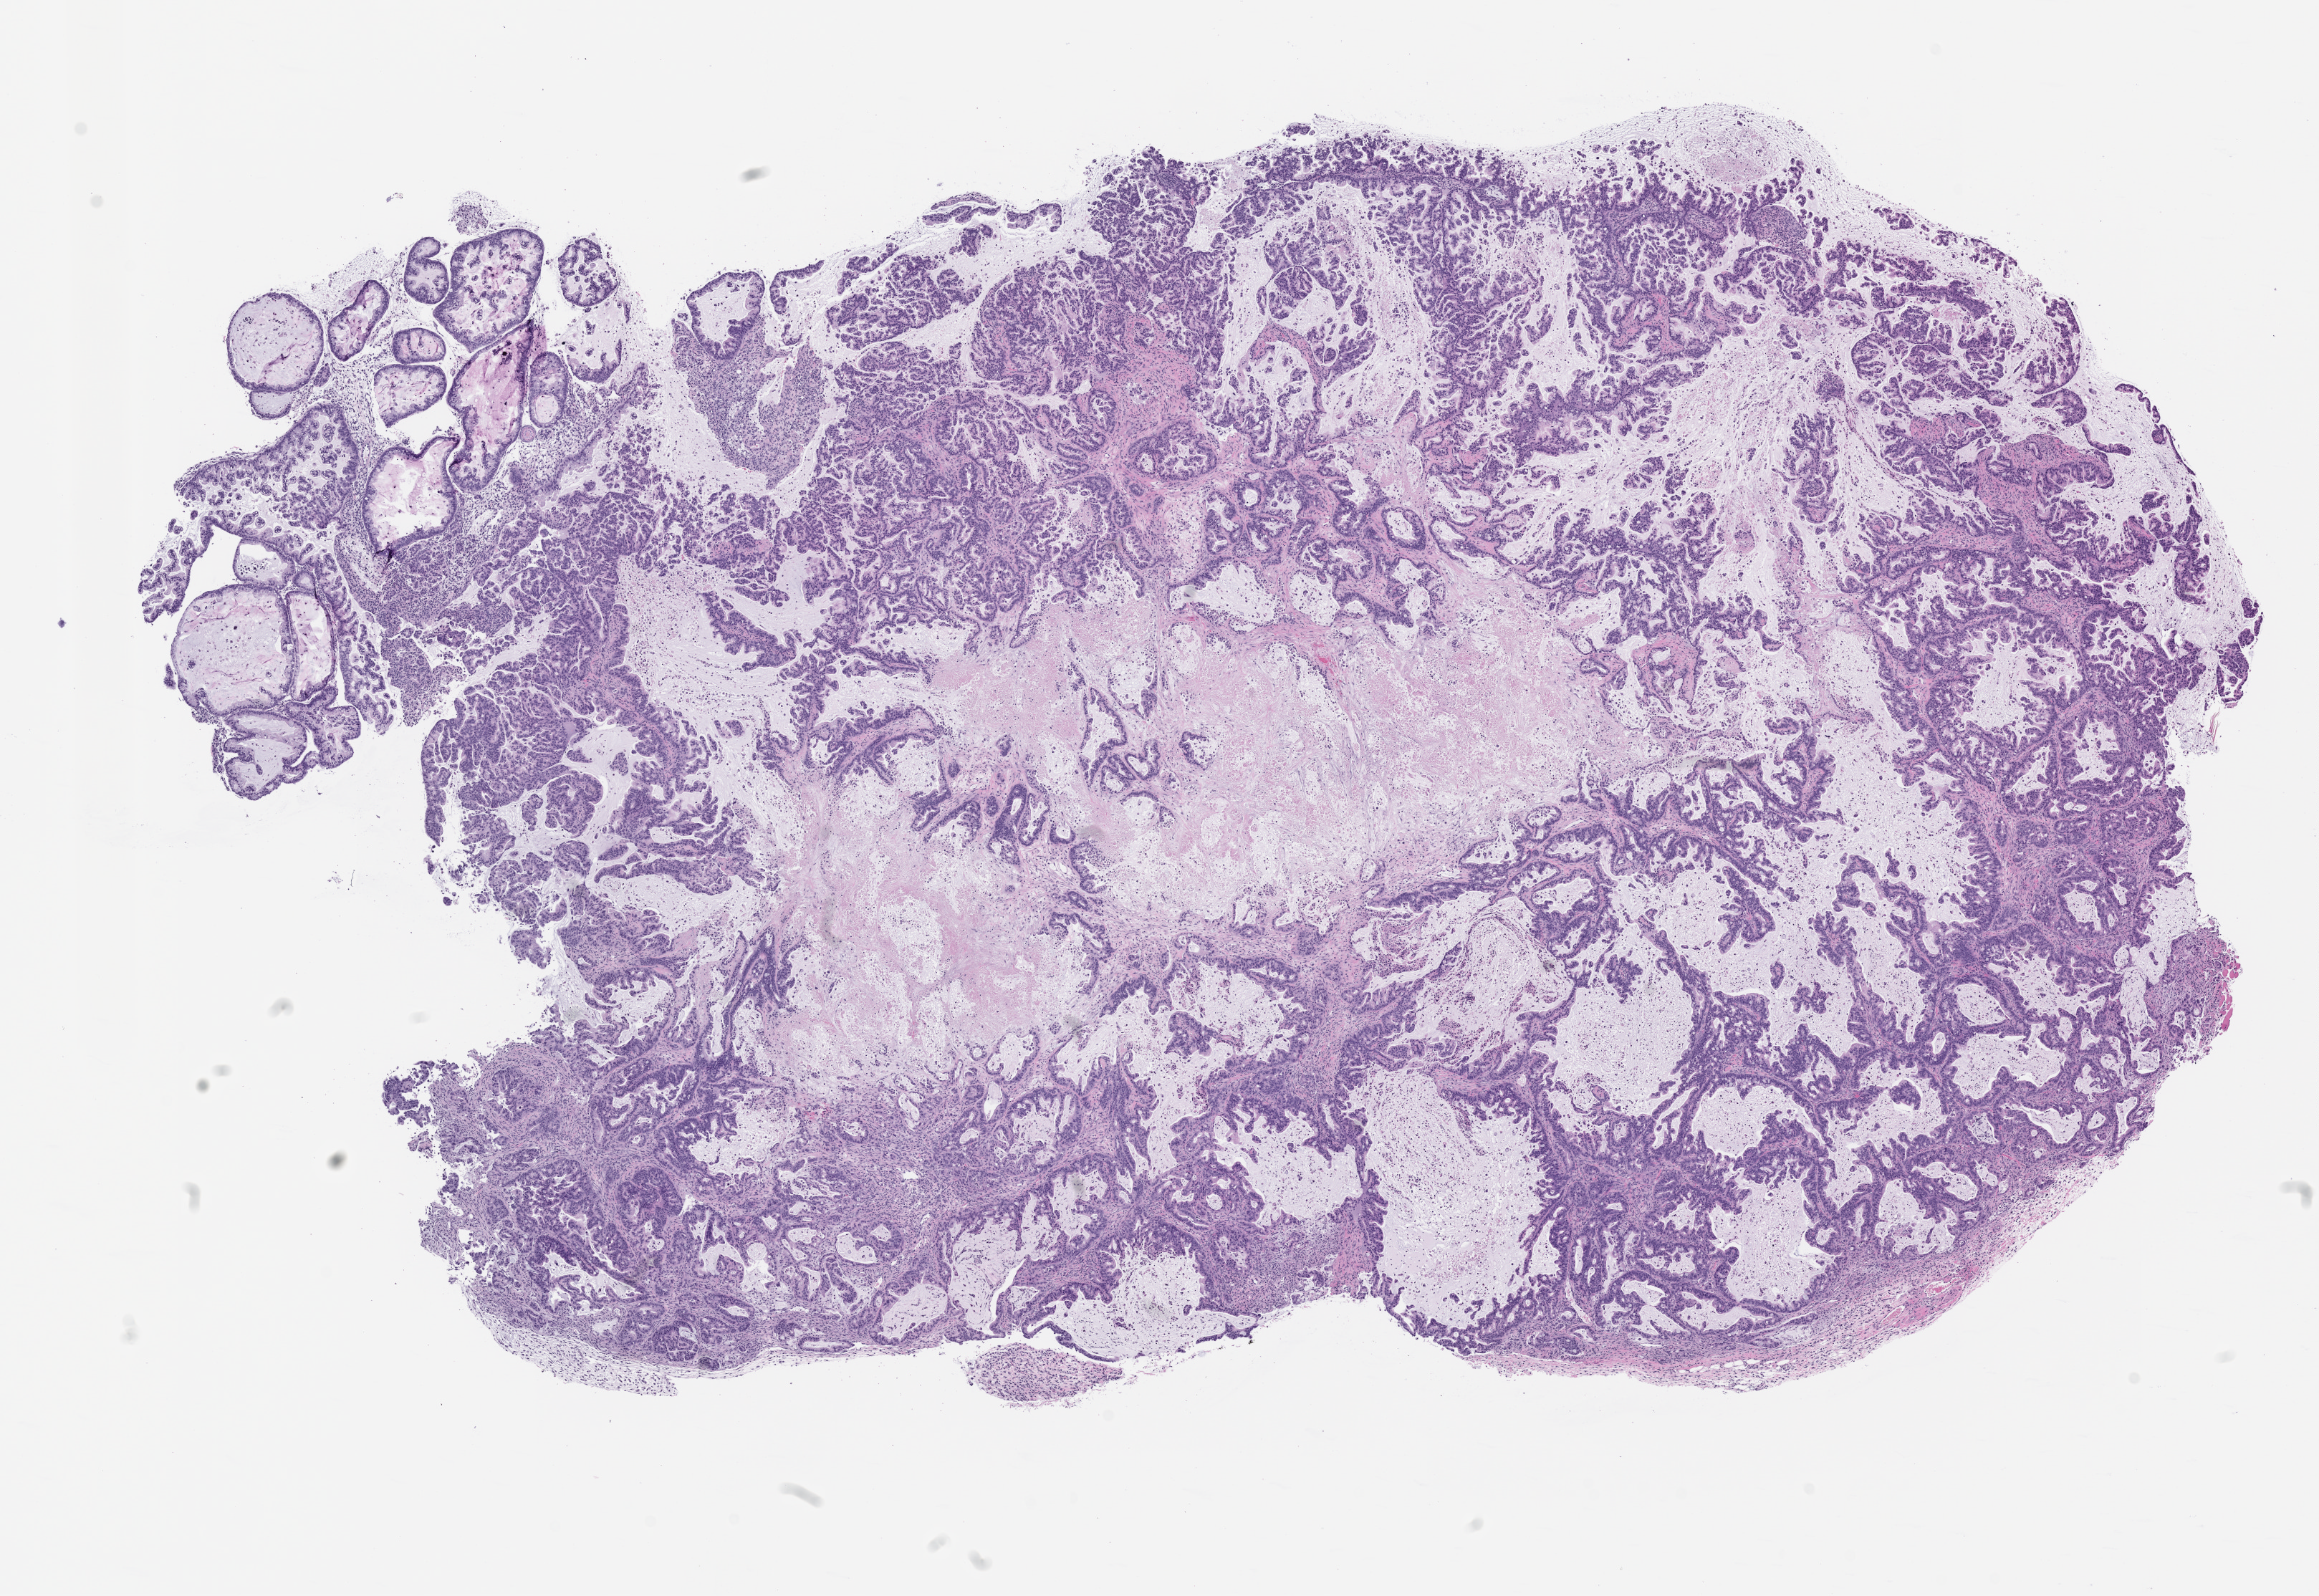
Whole-slide image, haematoxylin and eosin: patient-derived xenograft (human tumor grown in a mouse), passage 2, shown as a low-resolution overview of the whole scanned area (about 13.0 x 9.0 mm); formalin-fixed, paraffin-embedded (FFPE) tissue; tumor site category: pancreas.
Originating patient diagnosis: Pancreatic Adenocarcinoma.